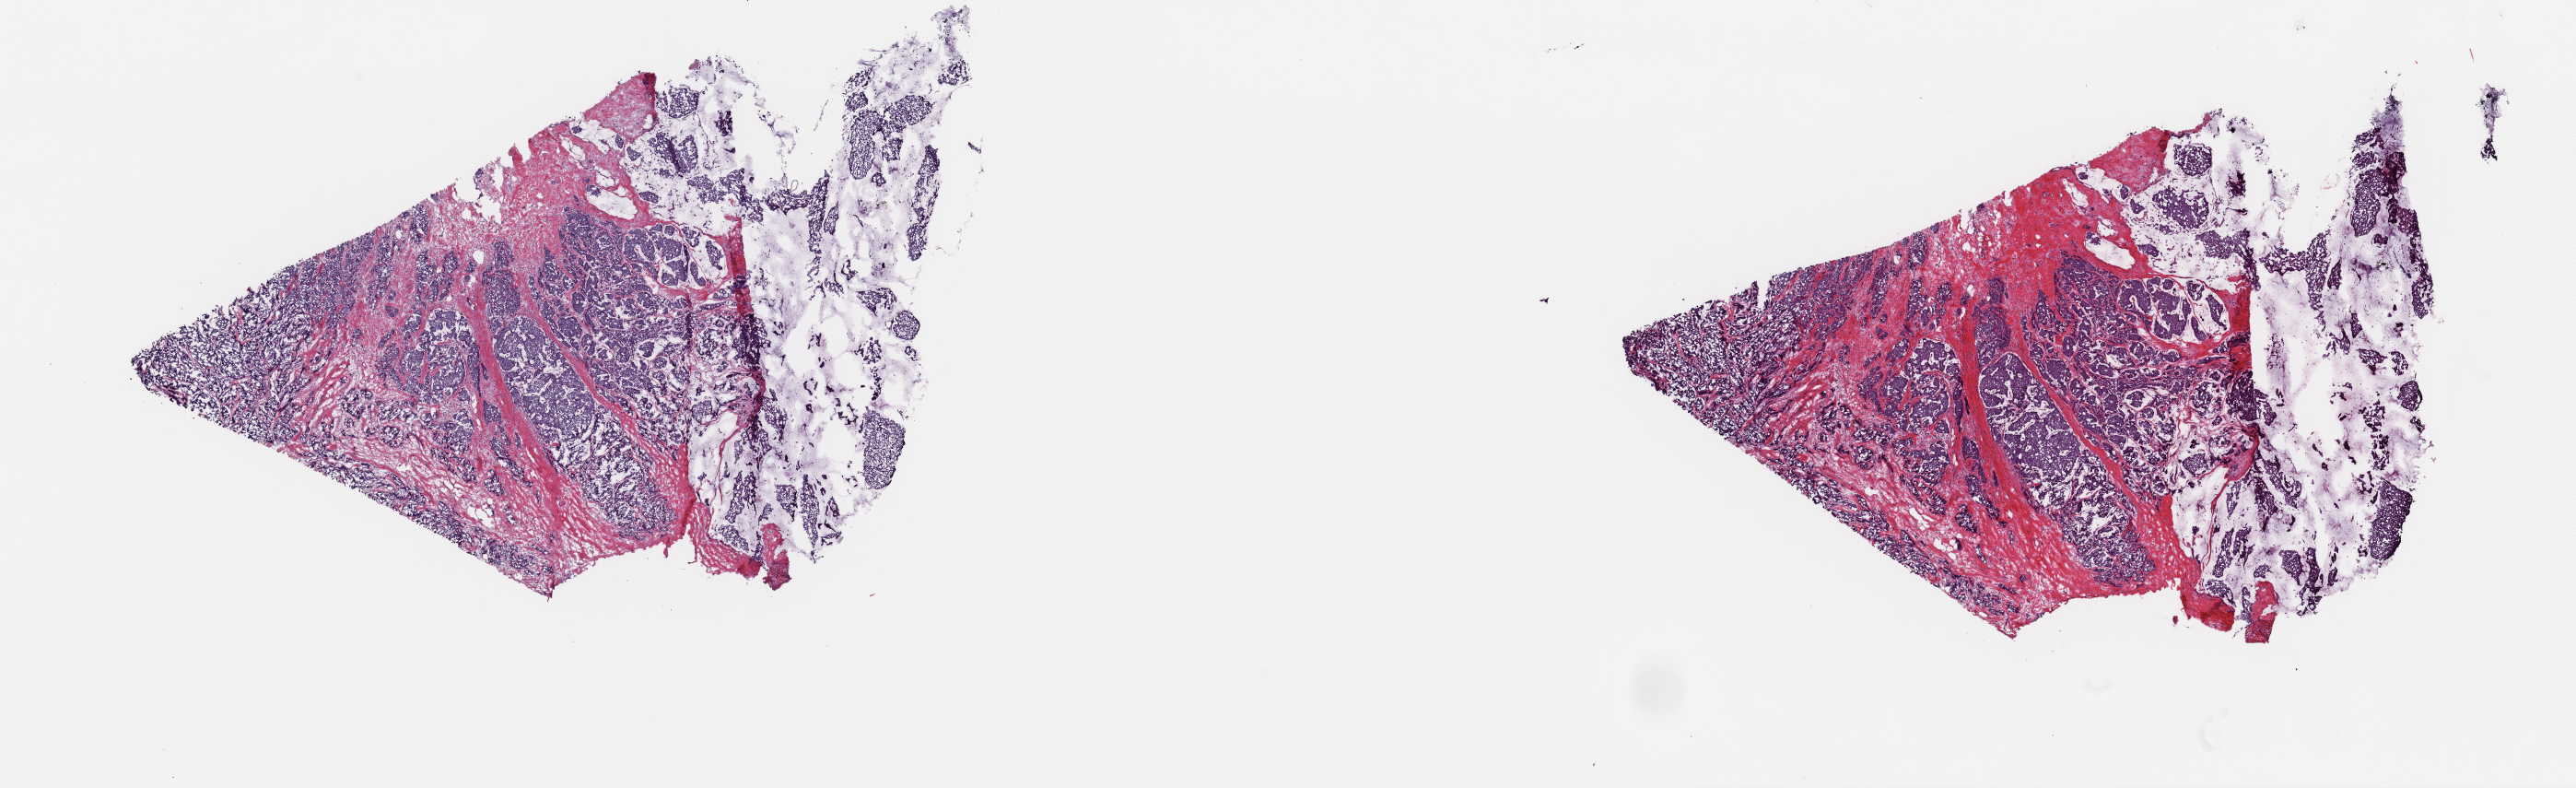
Digitized H&E tissue section (whole slide), shown as a low-resolution overview of the whole scanned area (about 22.1 x 6.8 mm), frozen section from the top of the tissue portion, sample: primary tumour, breast. Female patient; age at initial diagnosis 62 years. Slide review estimates, as recorded: tumour cells 95%, tumour nuclei 92%, normal cells 0%, stromal cells 5%, necrosis 0%. Infiltration values recorded for this section: lymphocyte infiltration 0%, monocyte infiltration 0%, neutrophil infiltration 0%.
Histologic diagnosis: Mucinous adenocarcinoma. Lymph nodes positive (case pathology): 0 of 2 examined. AJCC pathologic stage: IIA (7th edition). TNM: T2 N0 M0.